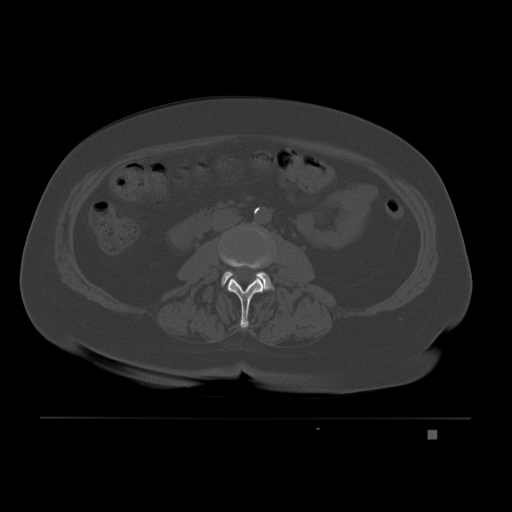
CT including the spine, one axial slice. Slice 57 of 221 in the series (ordered by position). Bone window (W 1800 / L 400 HU). 3 mm slice thickness. 512 × 512 image matrix, field of view 474 × 474 mm. Patient: female, 63 years. From the clinical record (not read from this slice): primary cancer: breast.
Annotated regions visible in this slice (semi-automatic segmentation, software-assisted and operator-edited):
- L2 vertebra: bounding box [x1, y1, x2, y2] px = [220, 249, 264, 328]
- L3 vertebra: [221, 271, 274, 291]